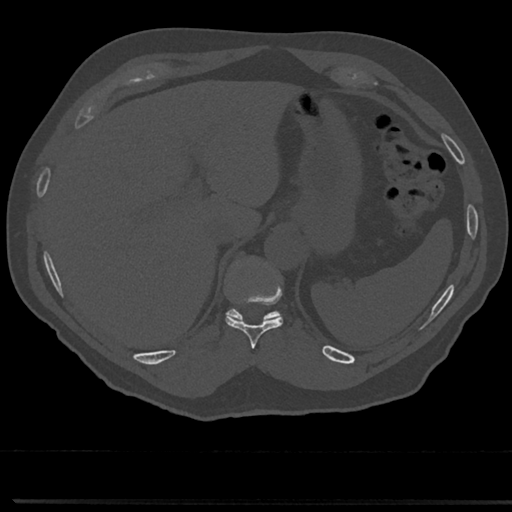
CT including the spine, one axial slice. Slice 241 of 817 in the series (ordered by position). Bone window (W 1800 / L 400 HU). 0.5 mm slice thickness. 512 × 512 image matrix, field of view 355 × 355 mm. Male patient, age 61 years. From the clinical record (not read from this slice): primary cancer: prostate.
Outlined on this slice (semi-automatically segmented with operator editing):
- T10 vertebra: bounding box <226,258,283,347> (left, top, right, bottom; pixels)
- T11 vertebra: <228,311,279,321>